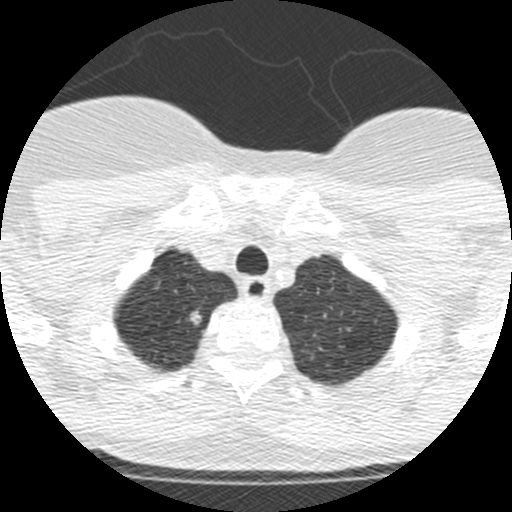
Low-dose screening chest CT, one axial slice; slice 217 of 250 in the series (ordered by position); reconstruction kernel STANDARD; 120 kVp; lung window (W 1500 / L -600 HU); 1.25 mm slice thickness; 512 × 512 image matrix, field of view 257 × 257 mm.
Outlined on this slice (manually delineated by an expert):
- lesion 1 (tumor, upper lobe of right lung): bounding box [x1, y1, x2, y2] px = [190, 311, 202, 325]